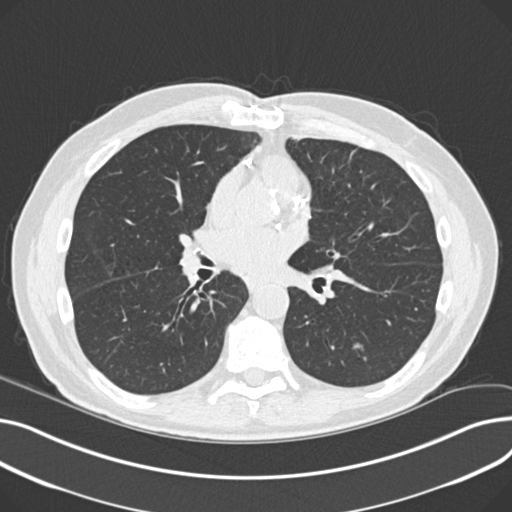
Low-dose screening chest CT, one axial slice. Position 109 of 230 along the scan axis. Lung window (W 1500 / L -600 HU). 2 mm slice thickness. 512 × 512 image matrix, field of view 372 × 372 mm.
Outlined on this slice (manually delineated by an expert):
- lesion 3 (nodule, lower lobe of left lung): box from (x=352, y=343) to (x=362, y=350) px